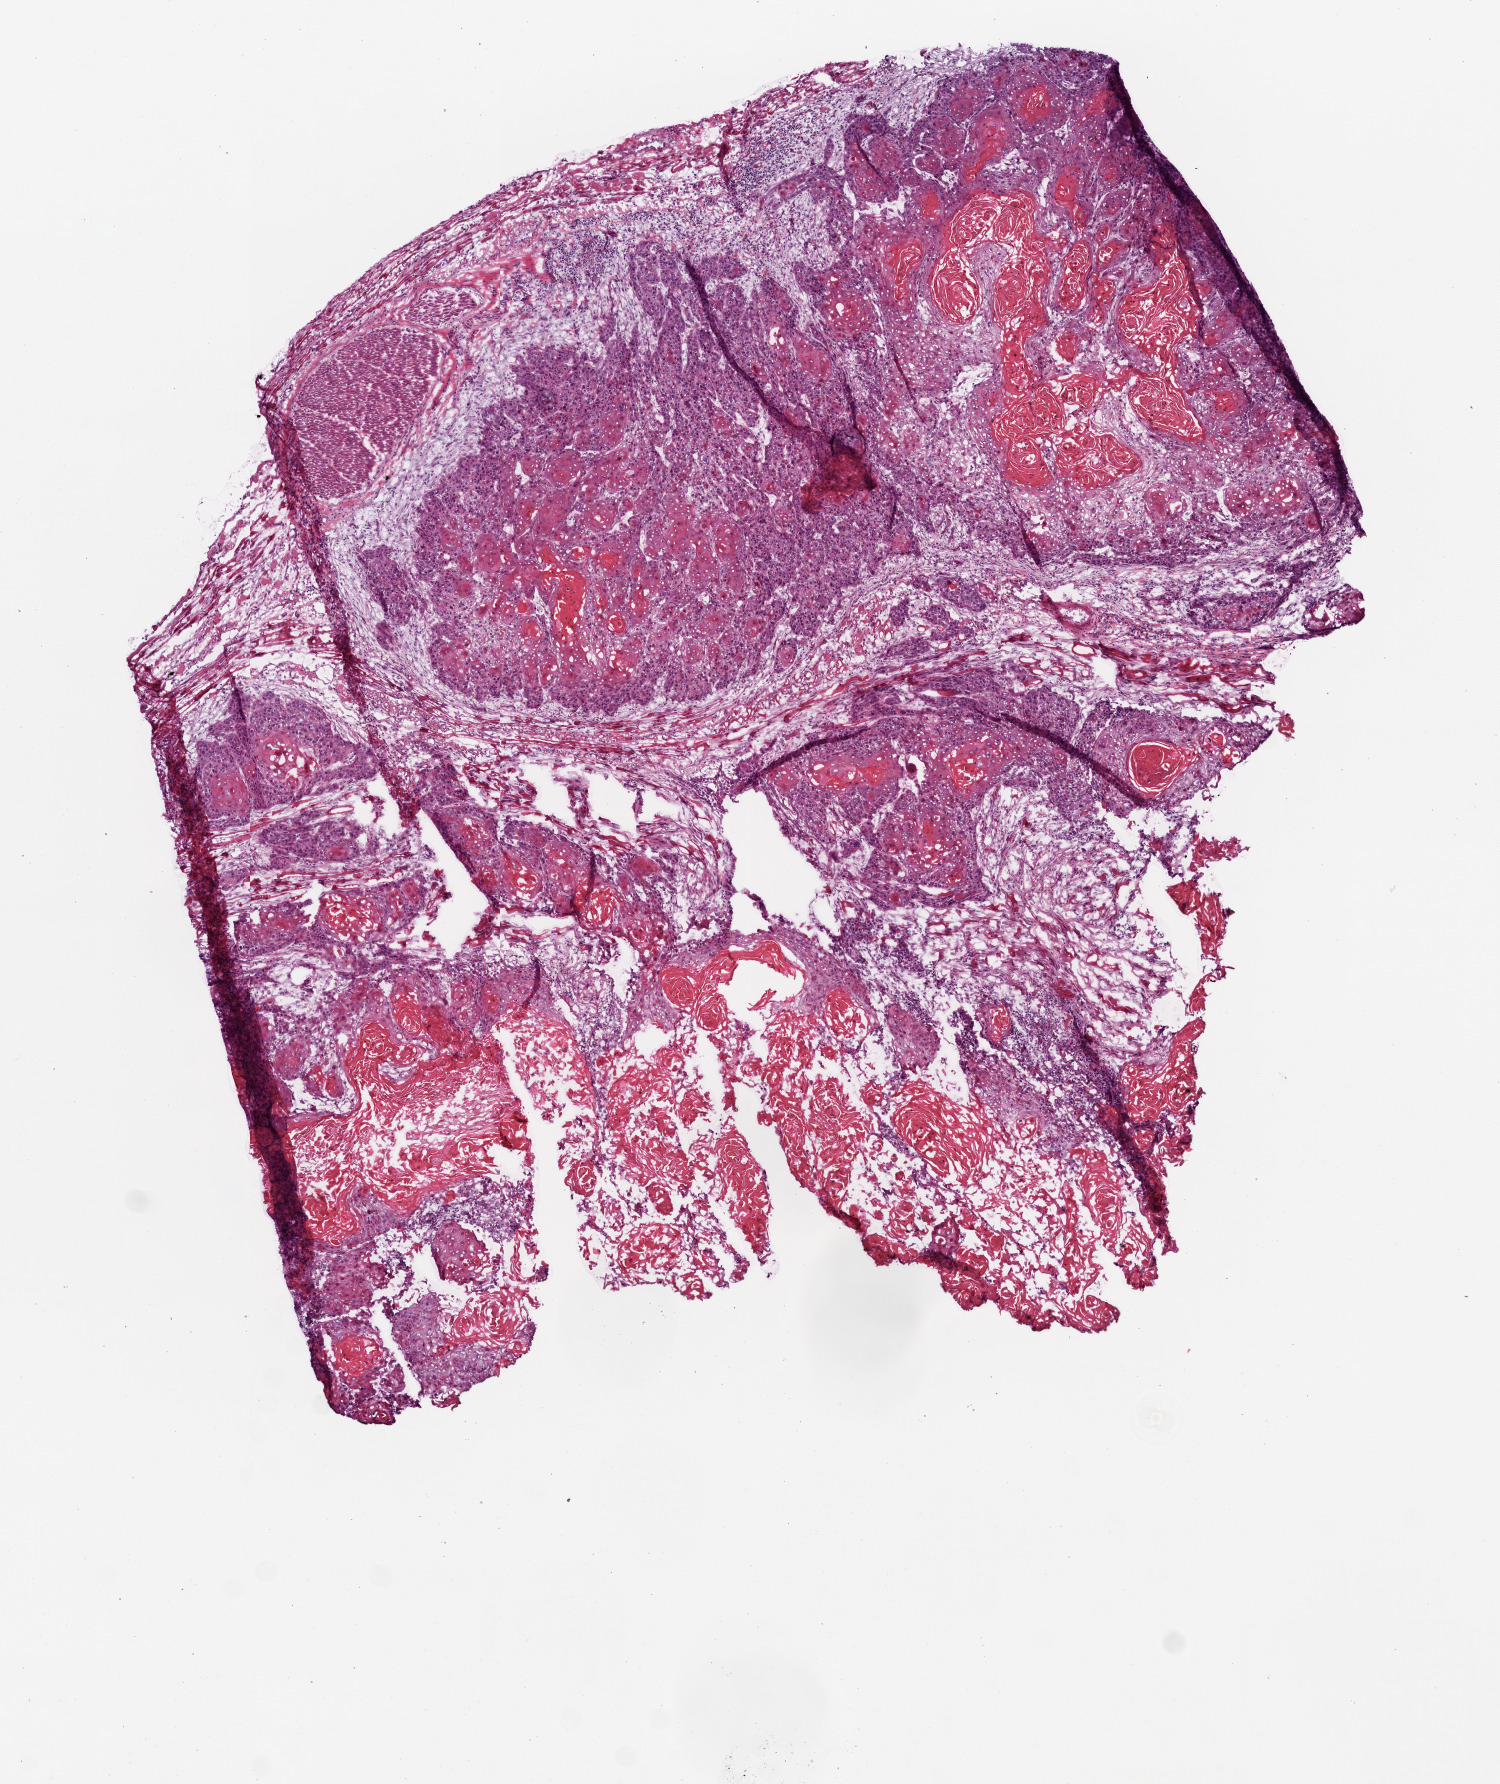
Whole-slide histology image, H&E, low-resolution overview of the scanned area, about 6.0 x 7.2 mm (from a 20x scan), frozen section from the top of the tissue portion, primary tumour sample from the head and neck. Male, age 19 years at initial diagnosis. Histologic grade: G2 (moderately differentiated). Slide review estimates, as recorded: tumour cells 85%, tumour nuclei 85%, normal cells 0%, stromal cells 15%, necrosis 0%.
Diagnosis: Squamous cell carcinoma, NOS (tongue, NOS). AJCC pathologic stage: IVA (7th edition).